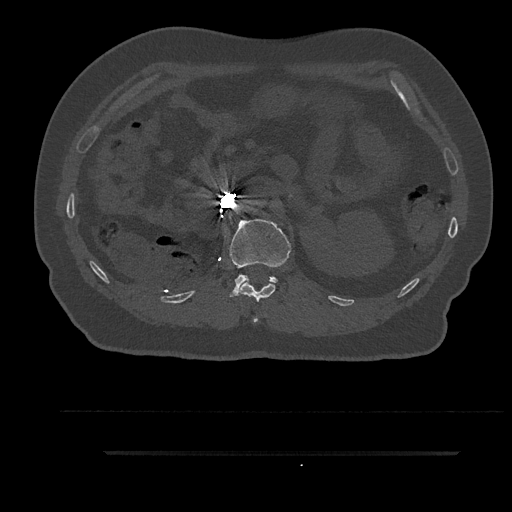
CT including the spine, one axial slice; slice 202 of 797 in the series (ordered by position); reconstruction kernel Br40s/3; bone window (W 1800 / L 400 HU); 512 × 512 image matrix, field of view 432 × 432 mm. Patient: male, 63 years. Case-level facts recorded for this patient, not image findings: primary cancer: renal; vertebrae with lytic lesions (as recorded): T8.
Structures marked on this image (semi-automatic segmentation, software-assisted and operator-edited):
- L1 vertebra: bounding box <229,219,291,297> (left, top, right, bottom; pixels)
- T12 vertebra: <239,281,276,323>